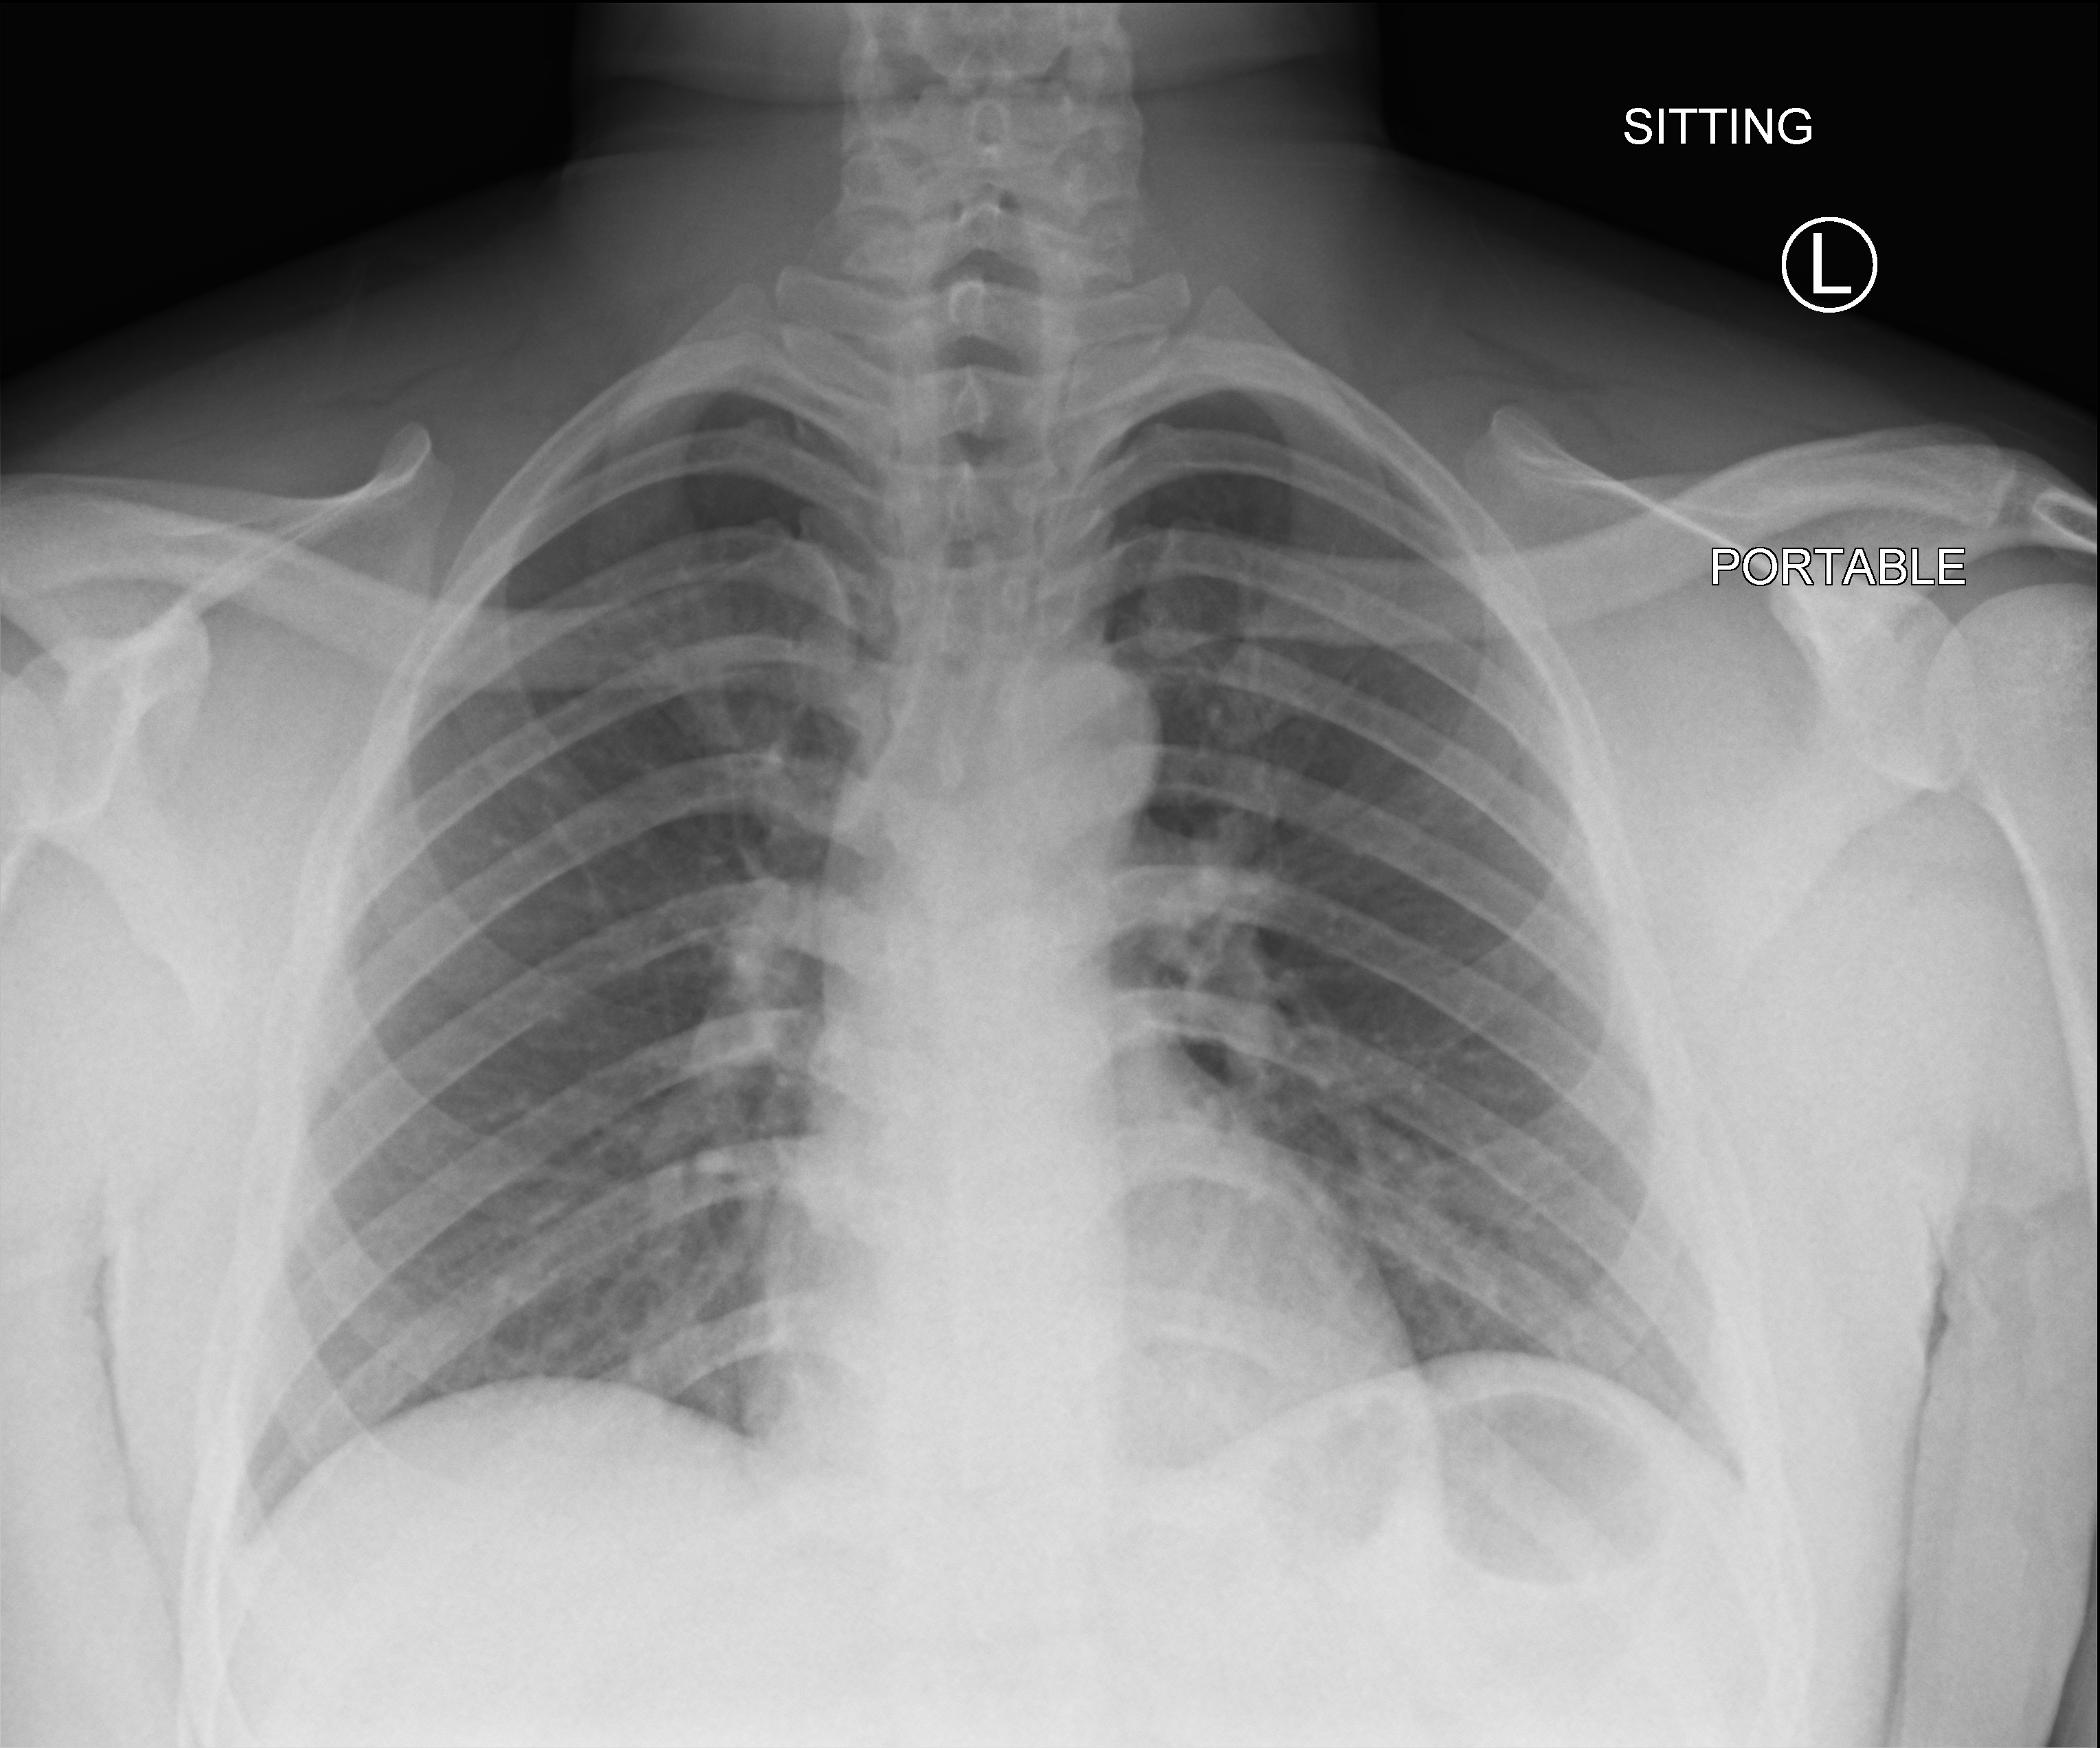
Bedside chest radiograph (computed radiography), anteroposterior (AP) projection. Male patient hospitalised with COVID-19, age 18–59 years.
Hospital-stay facts (about this admission, not read from this image; timing relative to this image not recorded): mechanically ventilated during this hospital stay: no.